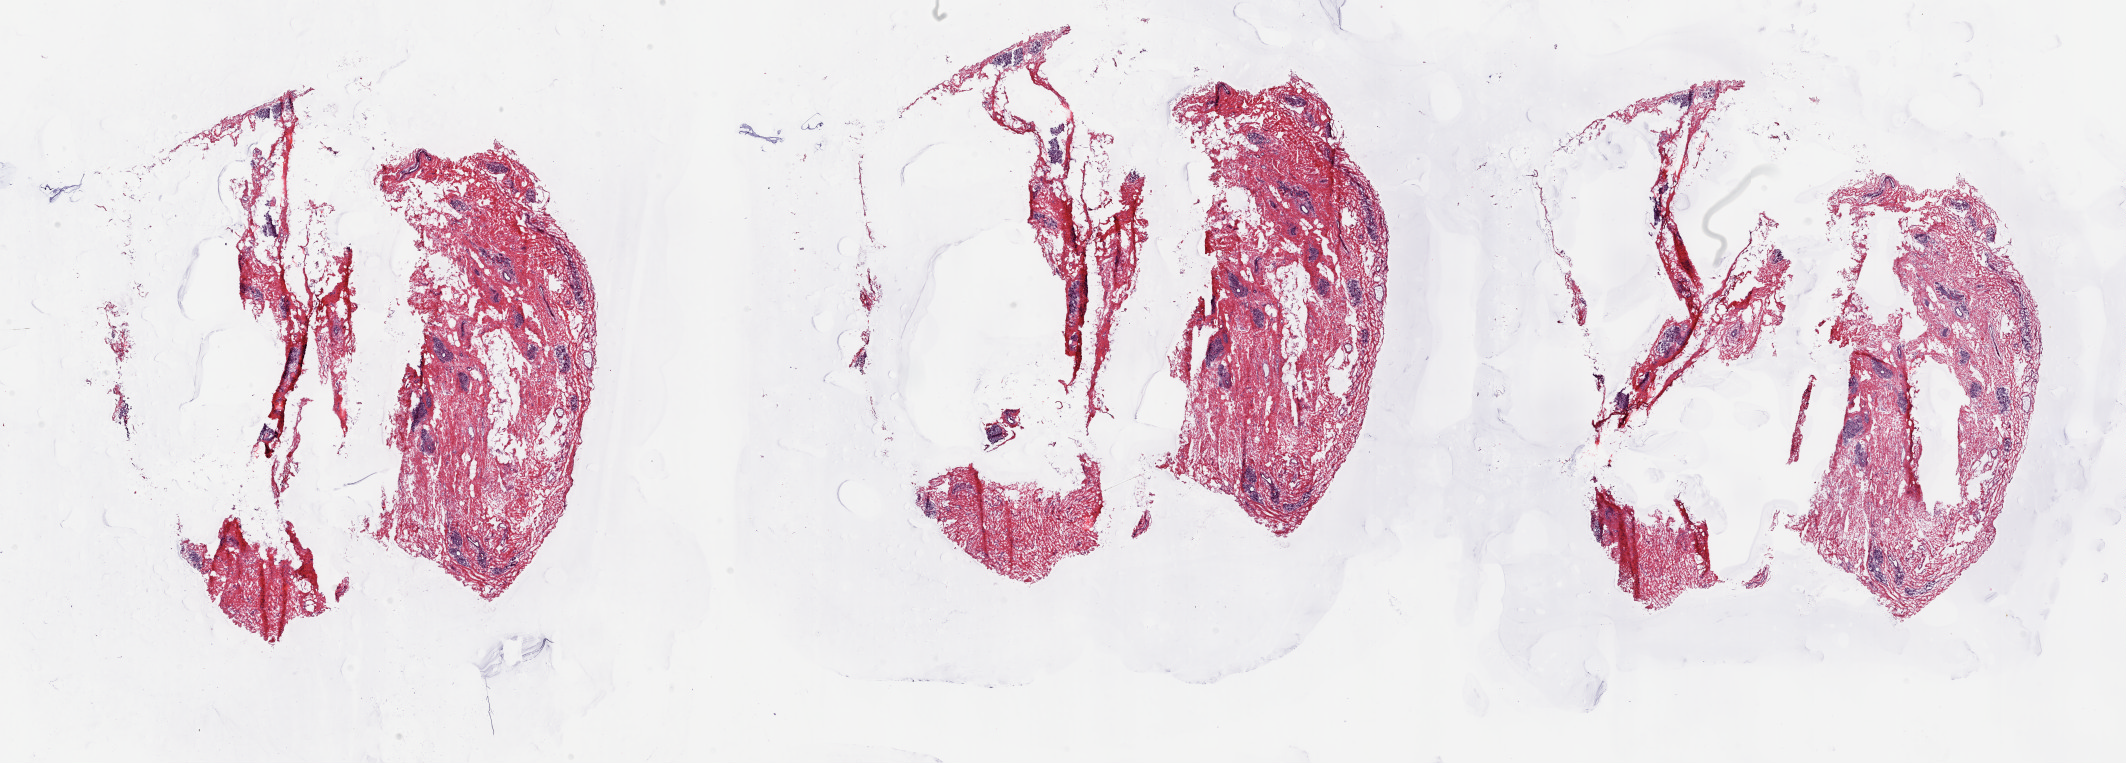
Digitized H&E-stained tissue section (whole slide) — whole scanned area (about 33.7 x 12.1 mm, from a 20x scan) shown as a low-resolution overview; frozen section from the top of the tissue portion; breast, solid tissue normal (non-tumour tissue) sample. Patient: female, age at initial diagnosis 52 years. Slide review estimates, as recorded: tumour cells 0%, tumour nuclei 0%.
This section: solid tissue normal (non-tumour) sample from the same patient. Patient diagnosis: Infiltrating duct carcinoma, NOS.